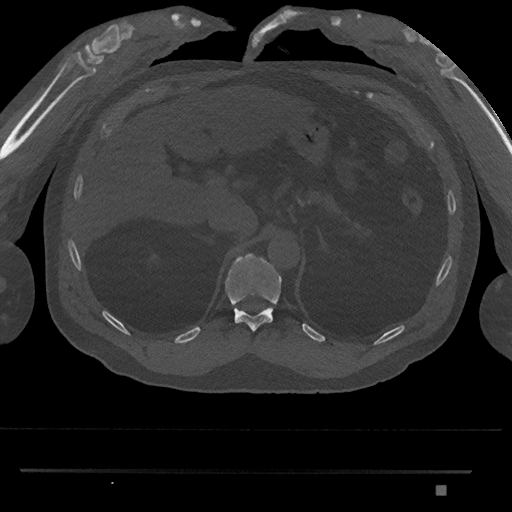
CT including the spine, one axial slice; position 942 of 1134 along the scan axis; reconstruction kernel Br40s/3; bone window (W 1800 / L 400 HU); 512 × 512 image matrix. Patient: male, 65 years. From the clinical record (not read from this slice): primary cancer: prostate.
Annotated regions visible in this slice (semi-automatically segmented with operator editing):
- T11 vertebra: bounding box [x1, y1, x2, y2] px = [225, 253, 282, 332]